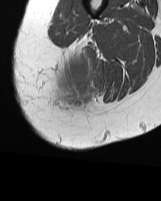
MRI of an extremity soft-tissue mass, one axial slice; position 13 of 70 along the scan axis; MR volume resampled by the dataset authors to the PET/CT grid (not the native acquisition matrix); 161 × 201 image matrix. Female patient. Case-level facts recorded for this patient, not image findings: histological type: synovial sarcoma; grade: intermediate; site of the primary tumour: right buttock.
Annotated regions visible in this slice (expert contour drawn on MRI and transferred to this co-registered scan by the dataset authors):
- gross tumour volume including surrounding oedema: box from (x=60, y=47) to (x=95, y=105) px
- gross tumour volume (mass): (x=60, y=61)–(x=91, y=105)